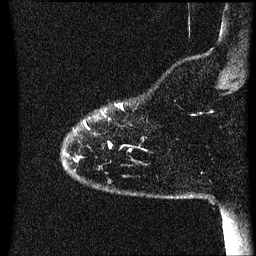
Breast MRI (dynamic contrast-enhanced), one sagittal slice; position 7 of 60 along the scan axis; dynamic contrast-enhanced series, image 2 of 3 at this slice position (ordered by acquisition); 1.5 T; TE 4.2 ms, TR 8.4 ms; 2.2 mm slice thickness; 256 × 256 image matrix. Patient: female, 35 years. From the clinical record (not read from this slice): setting: breast cancer imaged before/during neoadjuvant chemotherapy; receptor status: HER2-positive.
Annotated regions visible in this slice (semi-automatically segmented with operator editing):
- analysis volume of interest (the breast-tissue region the enhancement analysis was run in; not a lesion): bounding box (x1, y1, x2, y2) in pixels: (64, 104, 147, 171)
- tumour enhancement mask (voxels above the 70 % enhancement threshold inside the analysis volume of interest): (109, 144, 132, 151)